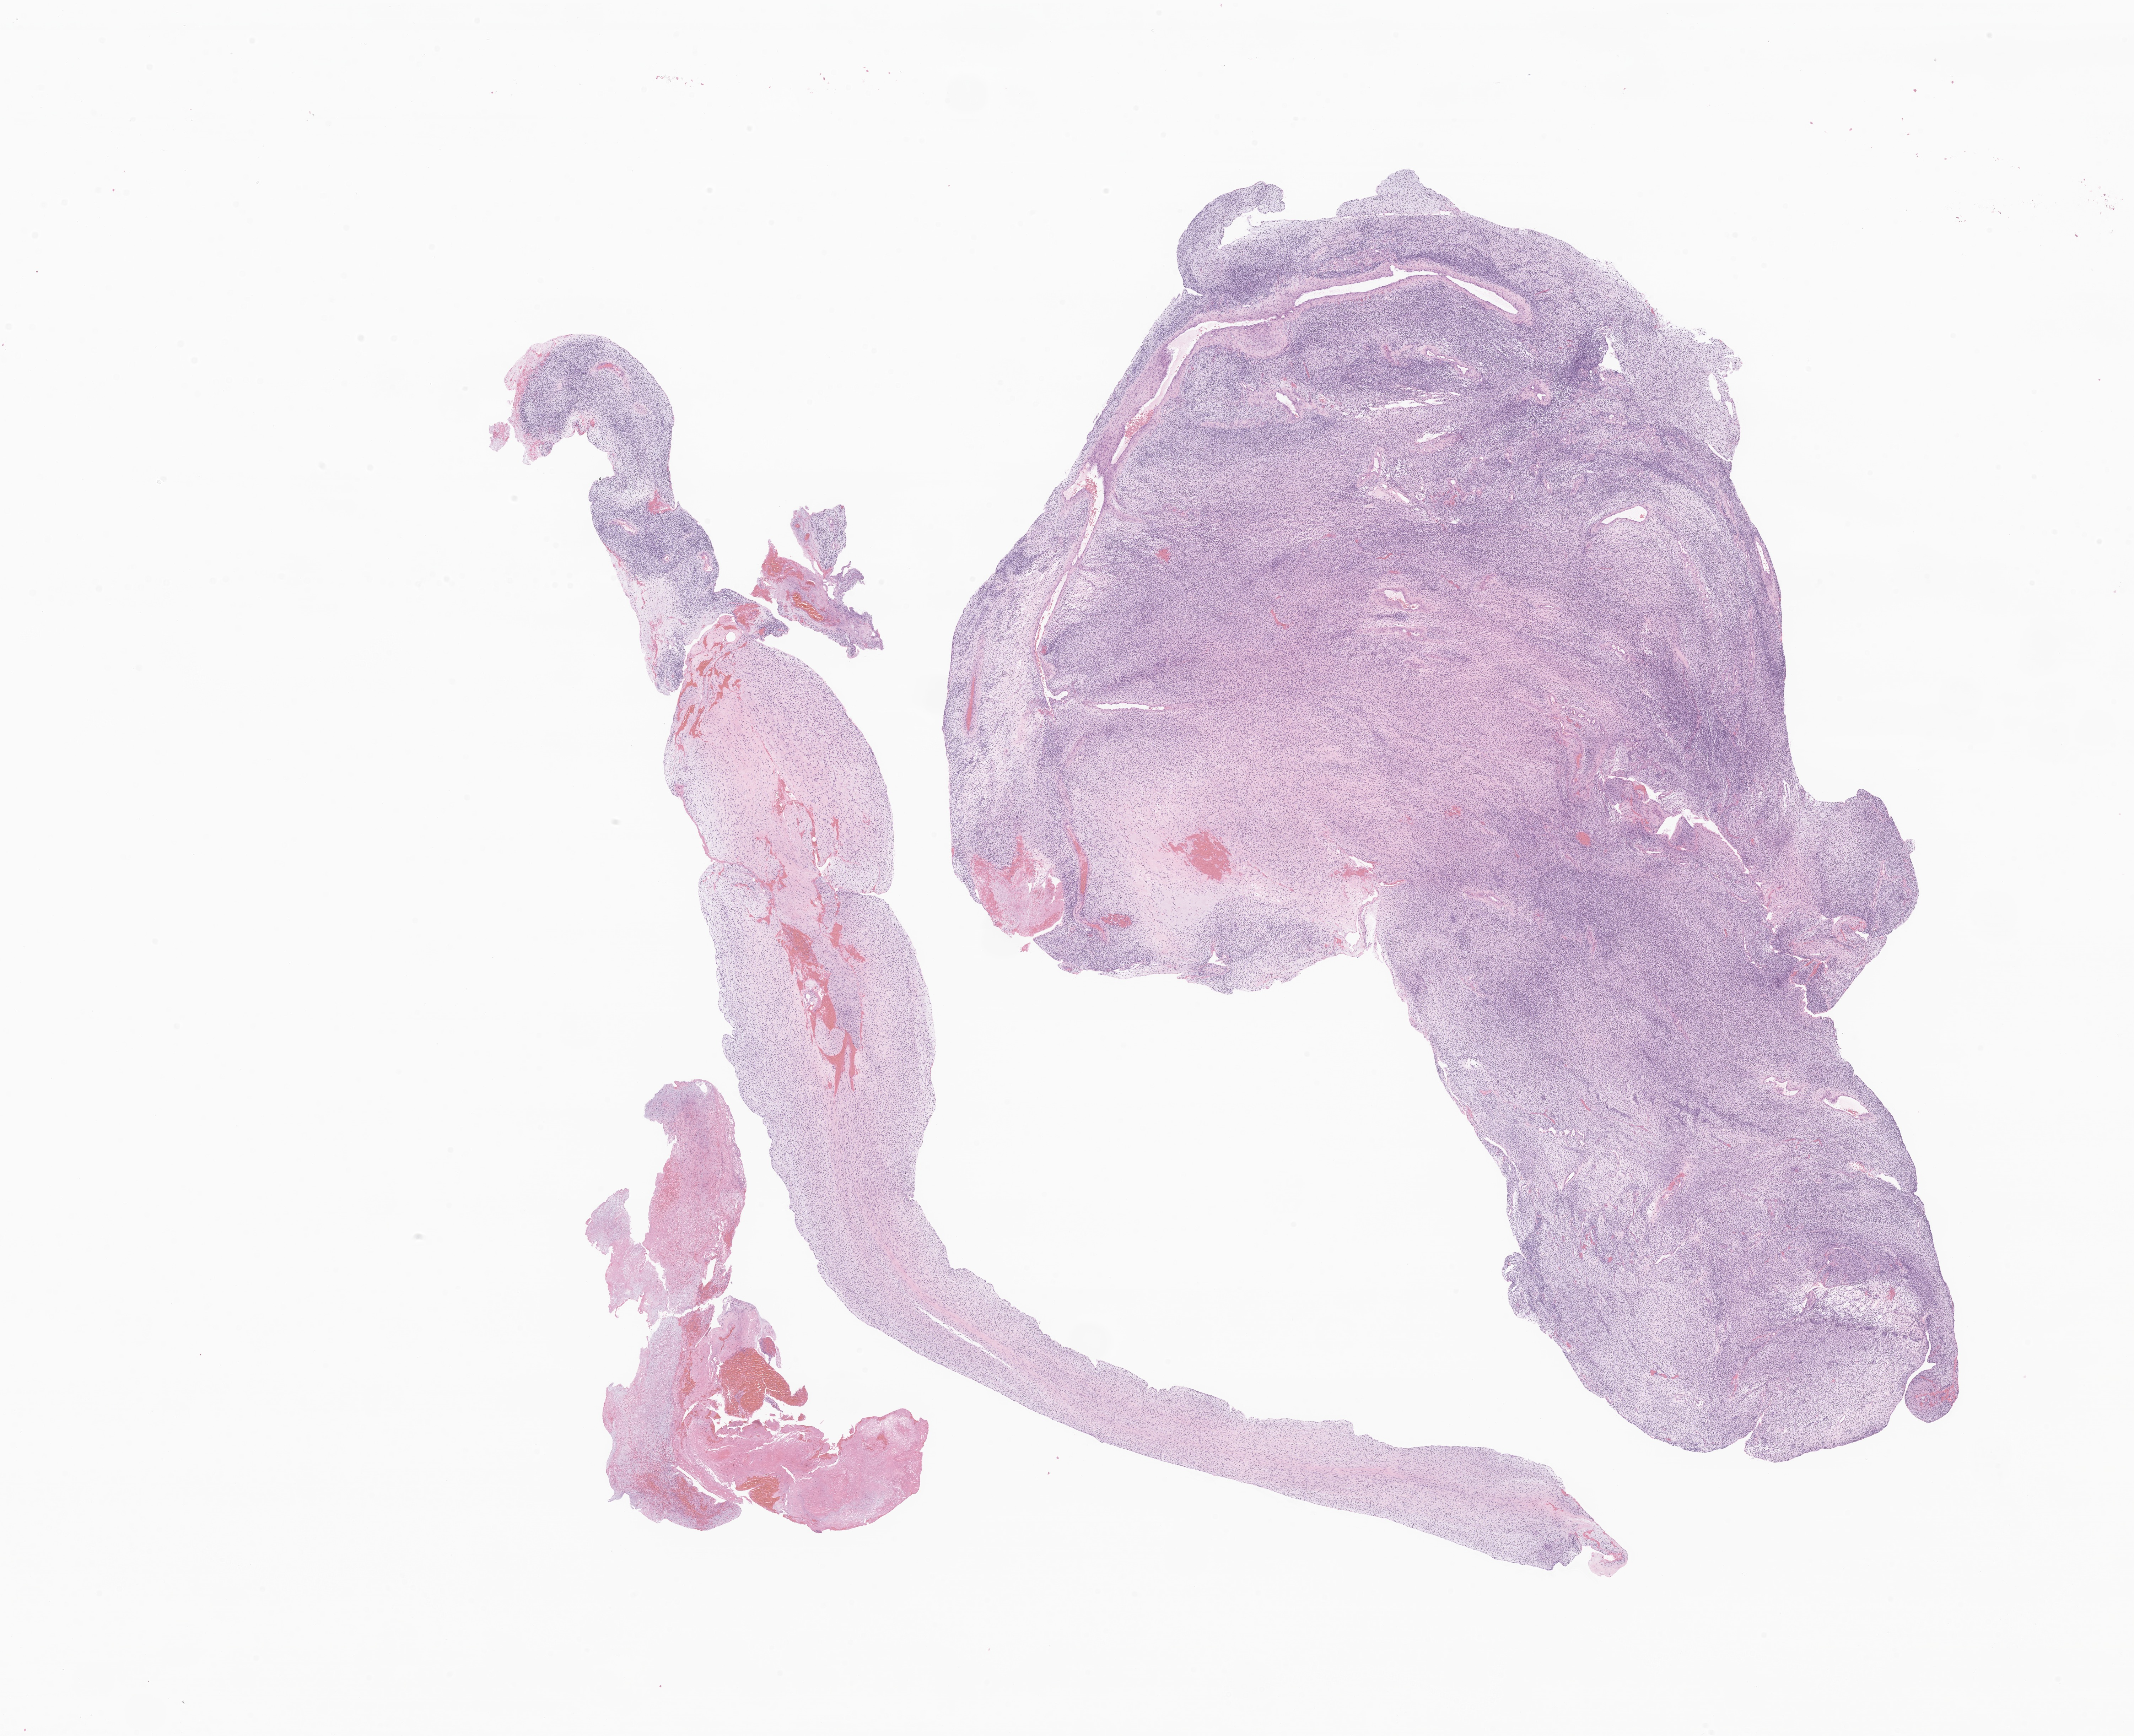
H&E whole-slide image of tumor tissue from the pelvis, low-resolution overview of the scanned area, about 25.3 x 20.6 mm, formalin-fixed, paraffin-embedded (FFPE) tissue. Male patient, age 223 months (18 years 7 months).
Recorded diagnosis: Rhabdomyosarcoma, NOS.